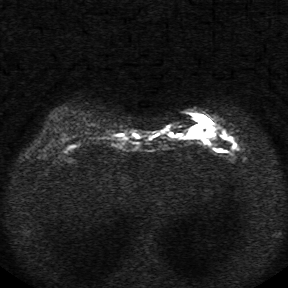
Breast MRI, one axial slice. Position 9 of 34 along the scan axis. Diffusion-weighted series; image 2 of 4 stored at this slice position (different b-values; order by instance number). 1.5 T. 5 mm slice thickness. 288 × 288 image matrix. Female patient.
Annotated regions visible in this slice (manually delineated by an expert):
- tumour on diffusion-weighted imaging: box from (x=189, y=116) to (x=216, y=137) px